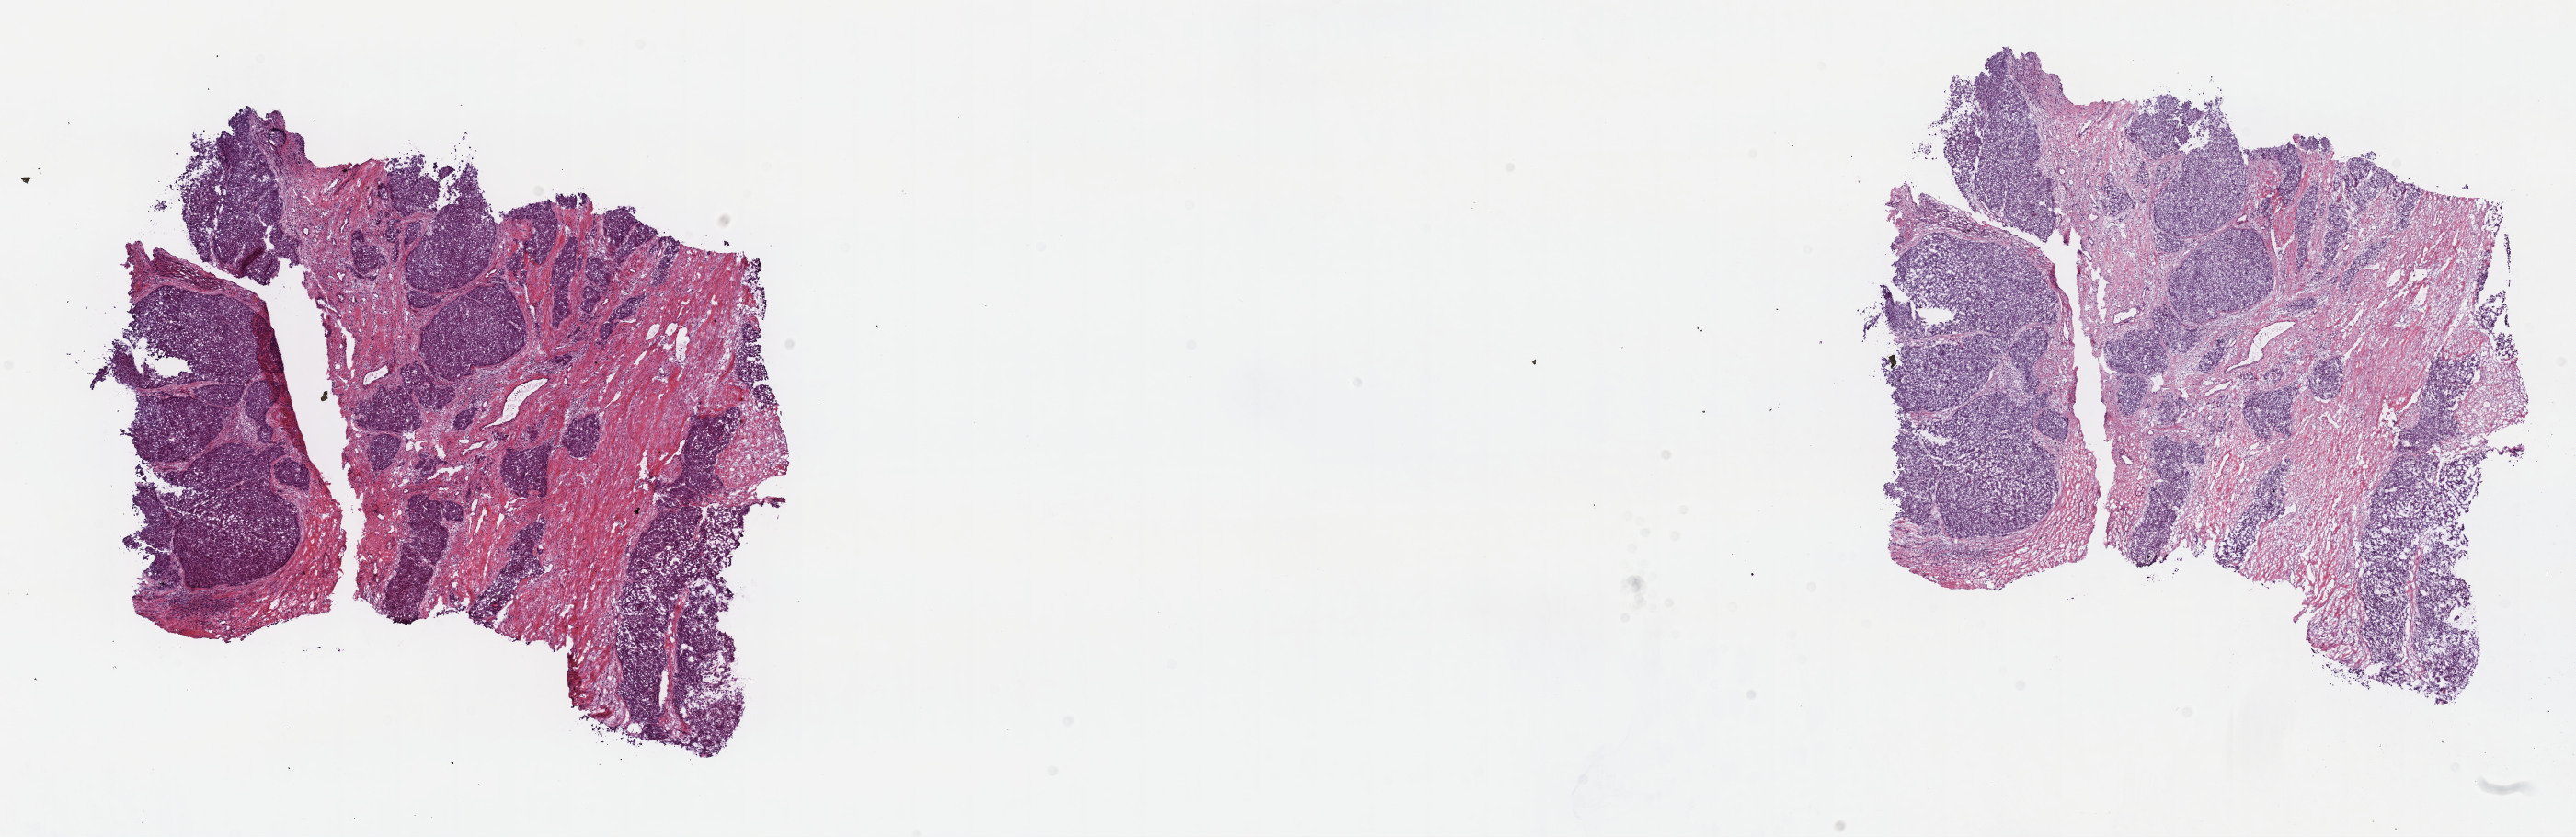
Digitized H&E-stained tissue section (whole slide), low-resolution overview of the scanned area, about 22.7 x 7.4 mm (acquisition: 40x scan), frozen section from the top of the tissue portion, sample: primary tumour, liver. Male patient; age at initial diagnosis 58 years. Histologic grade: G2 (moderately differentiated). Pathologist review of this section (percent, as recorded): tumour cells 50%, tumour nuclei 65%, normal cells 50%, stromal cells 0%, necrosis 0%. Inflammatory infiltration, as recorded: lymphocyte infiltration 5%, monocyte infiltration 0%, neutrophil infiltration 0%.
Histologic diagnosis: Hepatocellular carcinoma, NOS. AJCC pathologic stage: II. TNM: T2 N0 M0.